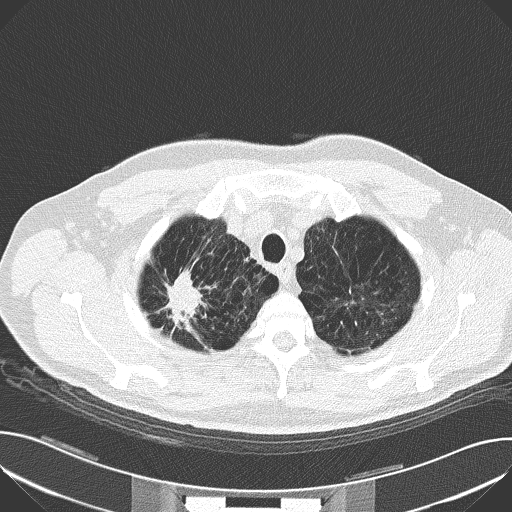
Low-dose screening chest CT, axial slice; baseline annual screen; lung window (W 1500 / L -600 HU); 512 × 512 image matrix, field of view 380 × 380 mm. Male, age 59 years at enrolment. Current smoker at enrolment.
Expert reader's lesion annotation, bounding box <155,260,221,330> (left, top, right, bottom; pixels). The screening reader recorded 4 non-calcified nodules or masses ≥4 mm on this exam (right upper lobe, left upper lobe, right upper lobe, left upper lobe); which of them this box marks is not recorded. Later outcome: lung cancer diagnosed 44 days after this screen — squamous cell carcinoma, NOS, right upper lobe, moderately differentiated (G2), stage IA (AJCC 6th edition), 30 mm at pathology.